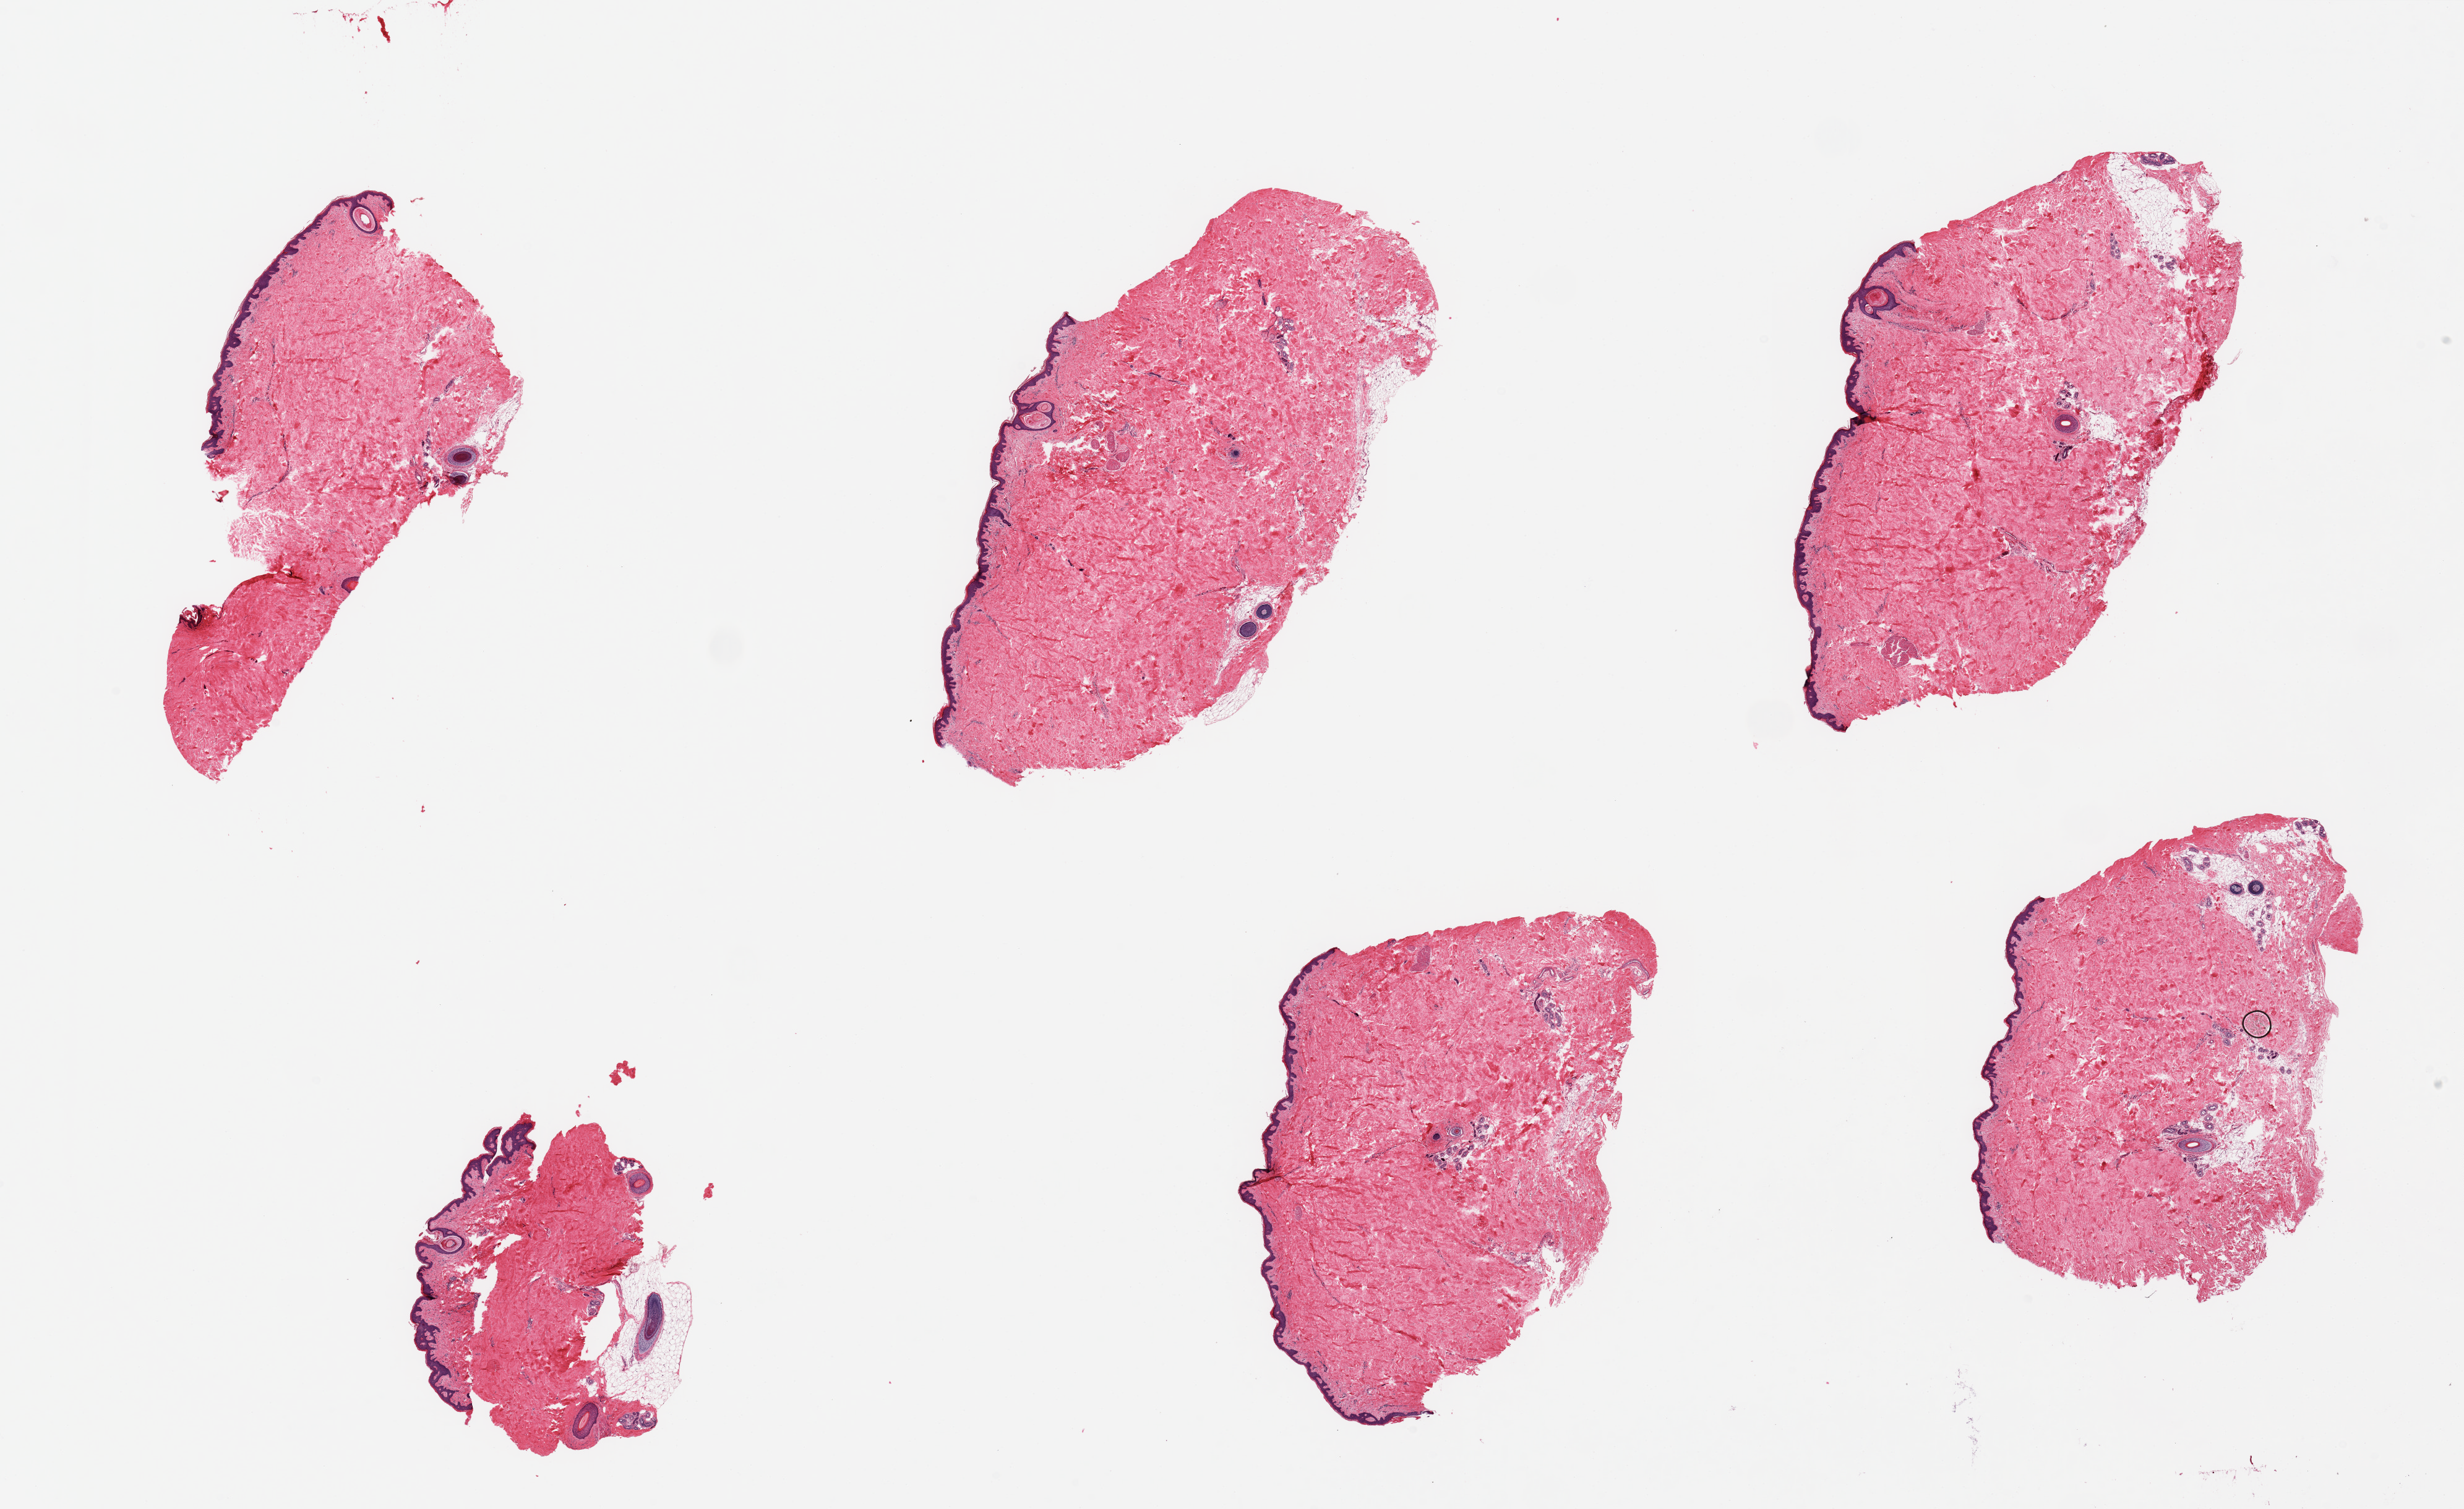
Digitized H&E-stained section, shown as a low-resolution overview of the whole scanned area (about 31.5 x 19.3 mm); PAXgene-fixed paraffin-embedded (PFPE) section; sampled site (target tissue): skin of suprapubic region; donor tissue sample. Male donor.
Review note (as recorded): 6 pieces, up to 8x4mm; all except the smallest are free of subcutaneous adipose.